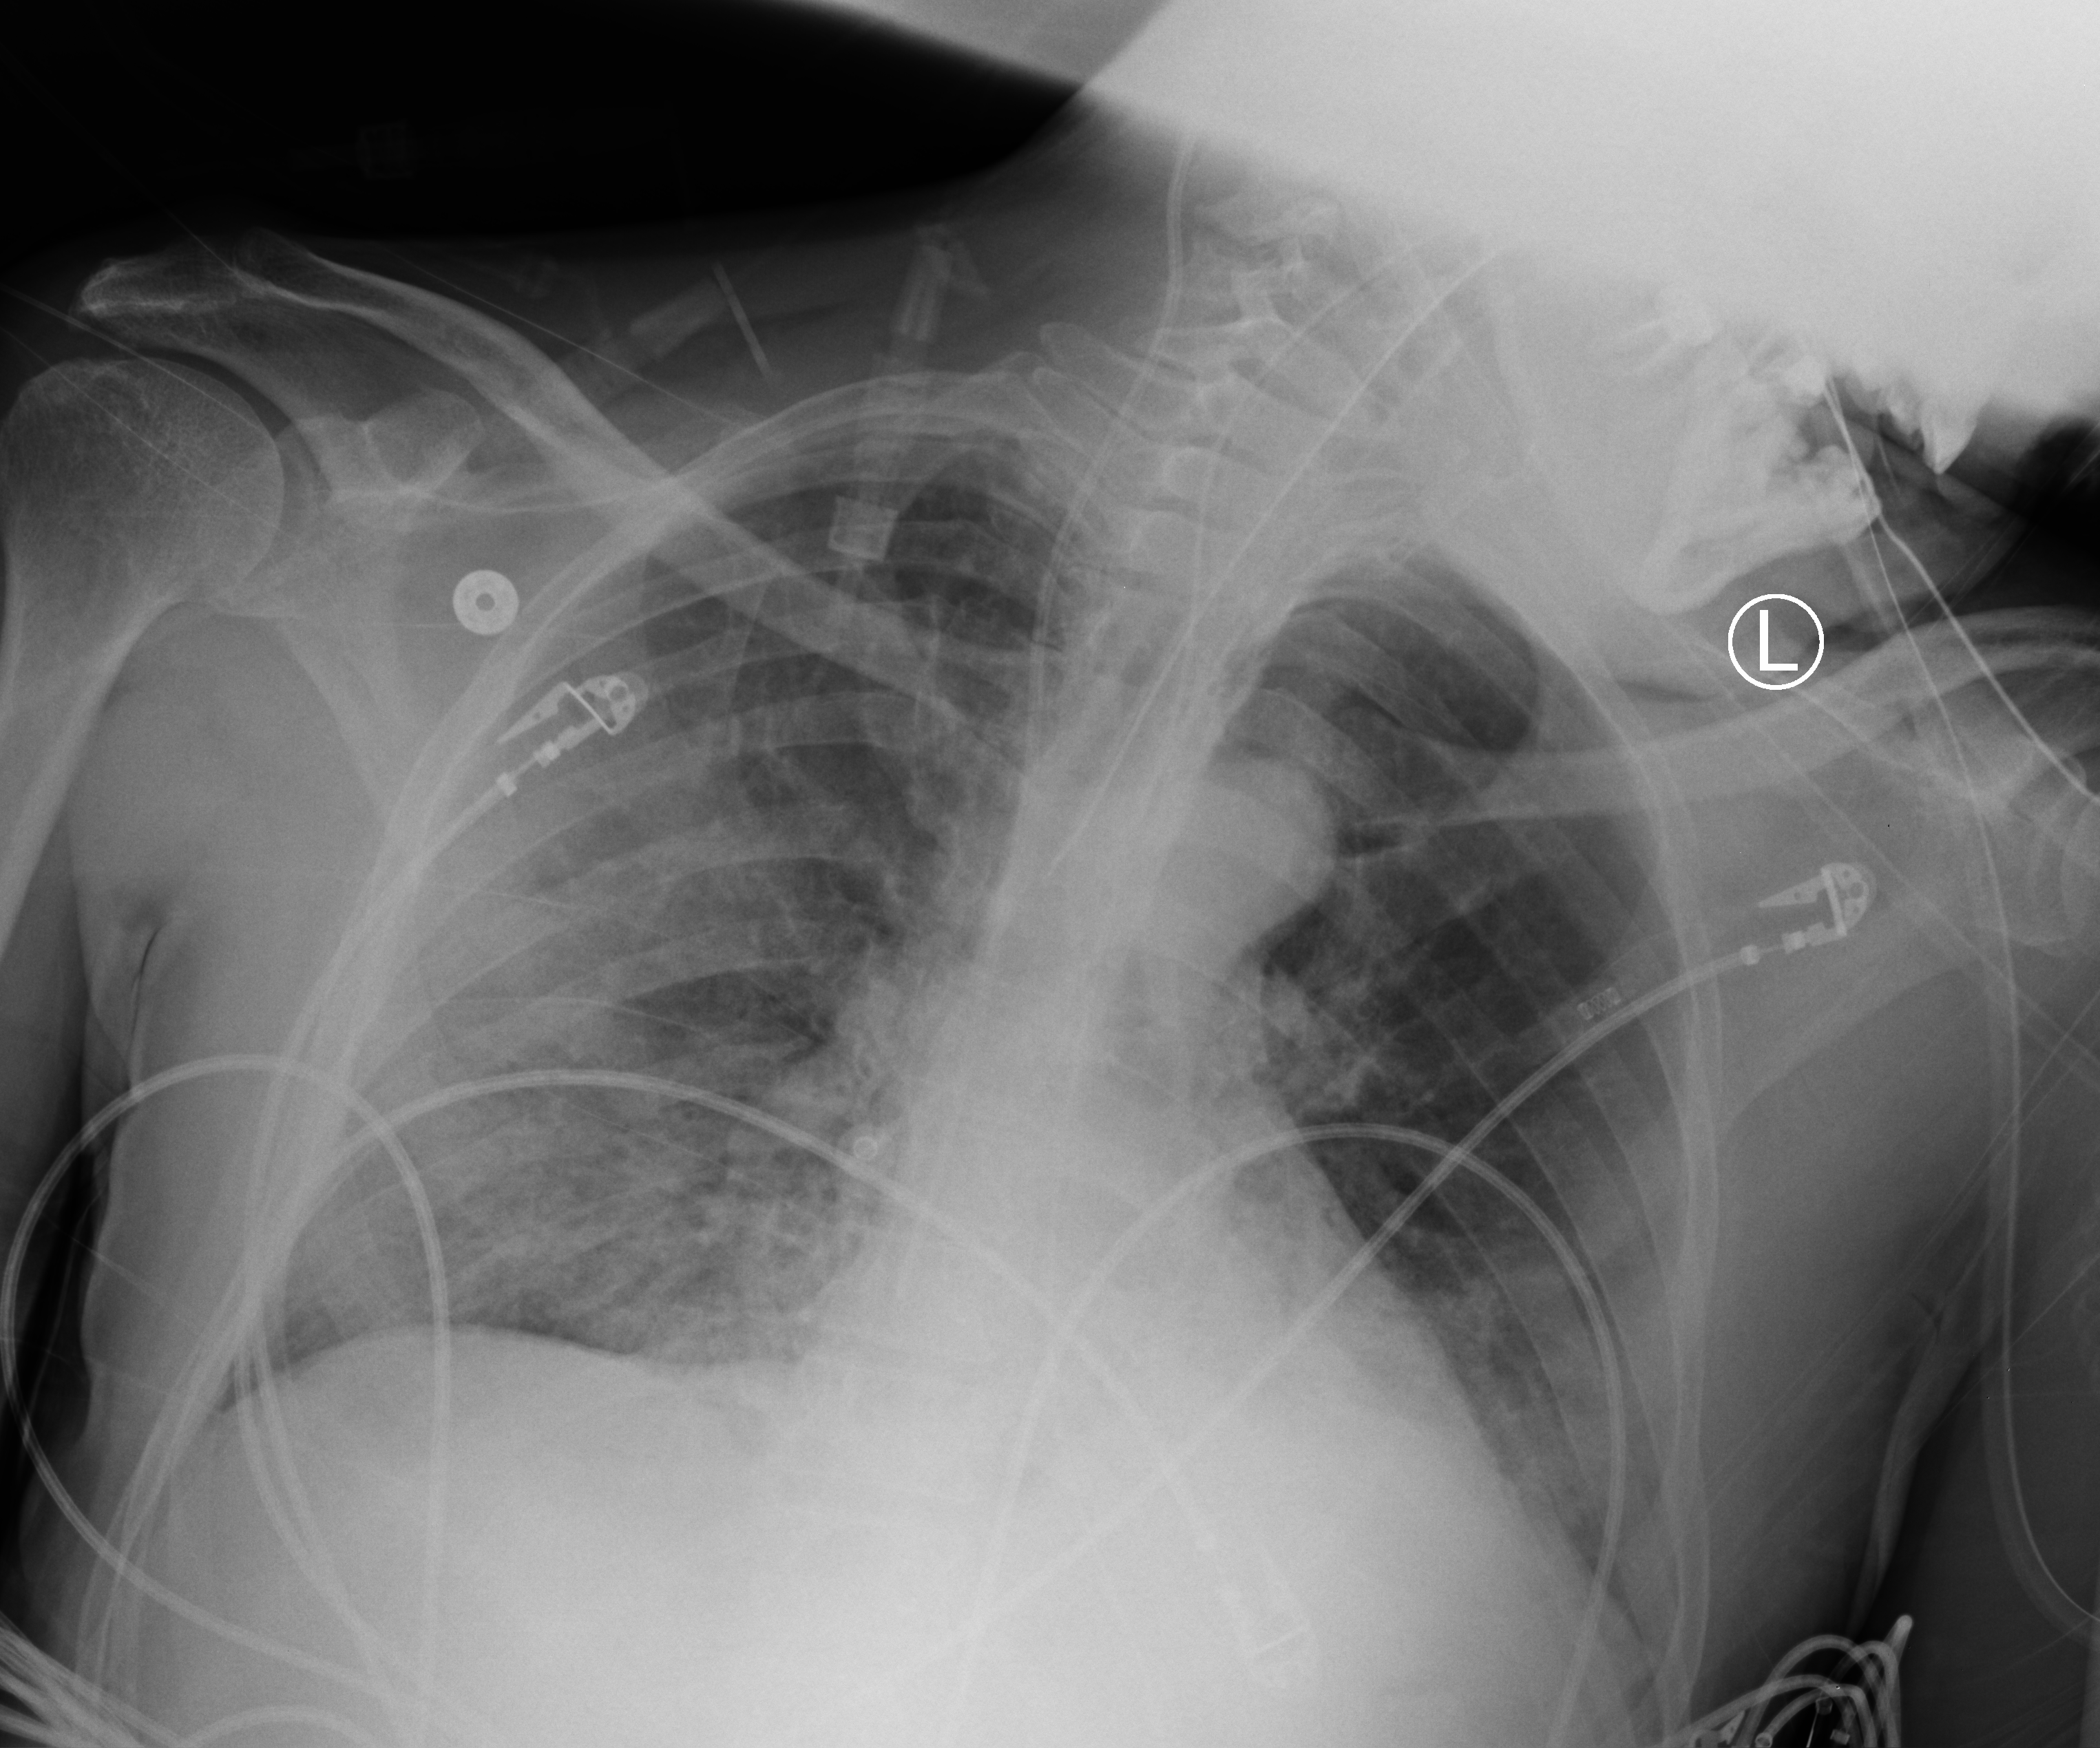
Bedside chest radiograph (computed radiography); anteroposterior (AP) projection. Male patient hospitalised with COVID-19, age 18–59 years.
From the hospital-stay record, not from the radiograph (when in the stay this image was taken is not recorded): COPD (admission record): no.